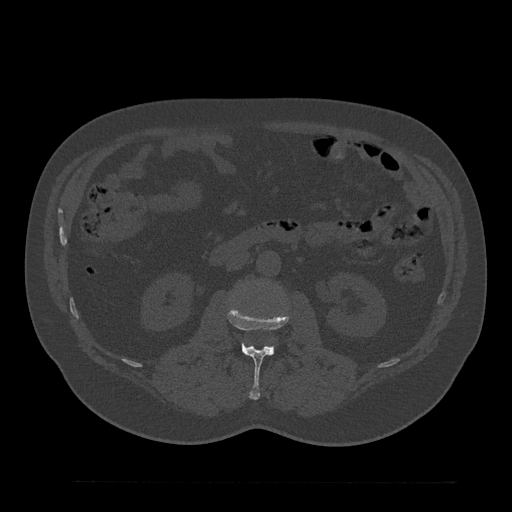
CT including the spine, one axial slice. Slice 83 of 797 in the series (ordered by position). Bone window (W 1800 / L 400 HU). 512 × 512 image matrix, field of view 430 × 430 mm. Patient: male, 61 years. From the clinical record (not read from this slice): primary cancer: prostate.
Annotated regions visible in this slice (semi-automatic segmentation, software-assisted and operator-edited):
- L2 vertebra: box from (x=227, y=306) to (x=289, y=400) px